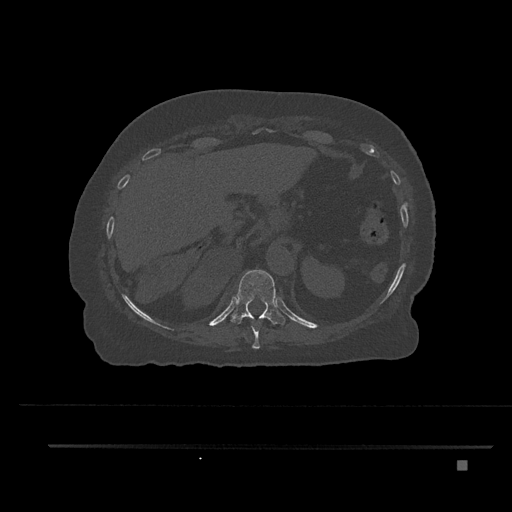
CT including the spine, one axial slice. Slice 321 of 797 in the series (ordered by position). Reconstruction kernel Br40s/3. Bone window (W 1800 / L 400 HU). 0.5 mm slice thickness. 512 × 512 image matrix. Female patient, age 76 years. From the clinical record (not read from this slice): primary cancer: lung.
Structures marked on this image (semi-automatic segmentation, software-assisted and operator-edited):
- T10 vertebra: bounding box <251,324,260,349> (left, top, right, bottom; pixels)
- T11 vertebra: <231,270,285,325>